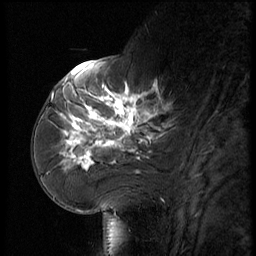
Breast MRI (dynamic contrast-enhanced), one sagittal slice; position 24 of 56 along the scan axis; dynamic contrast-enhanced series, image 2 of 3 at this slice position (ordered by acquisition); 1.5 T; TE 4.2 ms, TR 9 ms; 2.5 mm slice thickness; 256 × 256 image matrix. Patient: female, 61 years. Case-level facts recorded for this patient, not image findings: setting: breast cancer imaged before/during neoadjuvant chemotherapy; receptor status: HR-positive, HER2-negative.
Annotated regions visible in this slice (semi-automatically segmented with operator editing):
- analysis volume of interest (the breast-tissue region the enhancement analysis was run in; not a lesion): bounding box (x1, y1, x2, y2) in pixels: (65, 74, 185, 175)
- tumour enhancement mask (voxels above the 140 % enhancement threshold inside the analysis volume of interest): (65, 83, 160, 168)